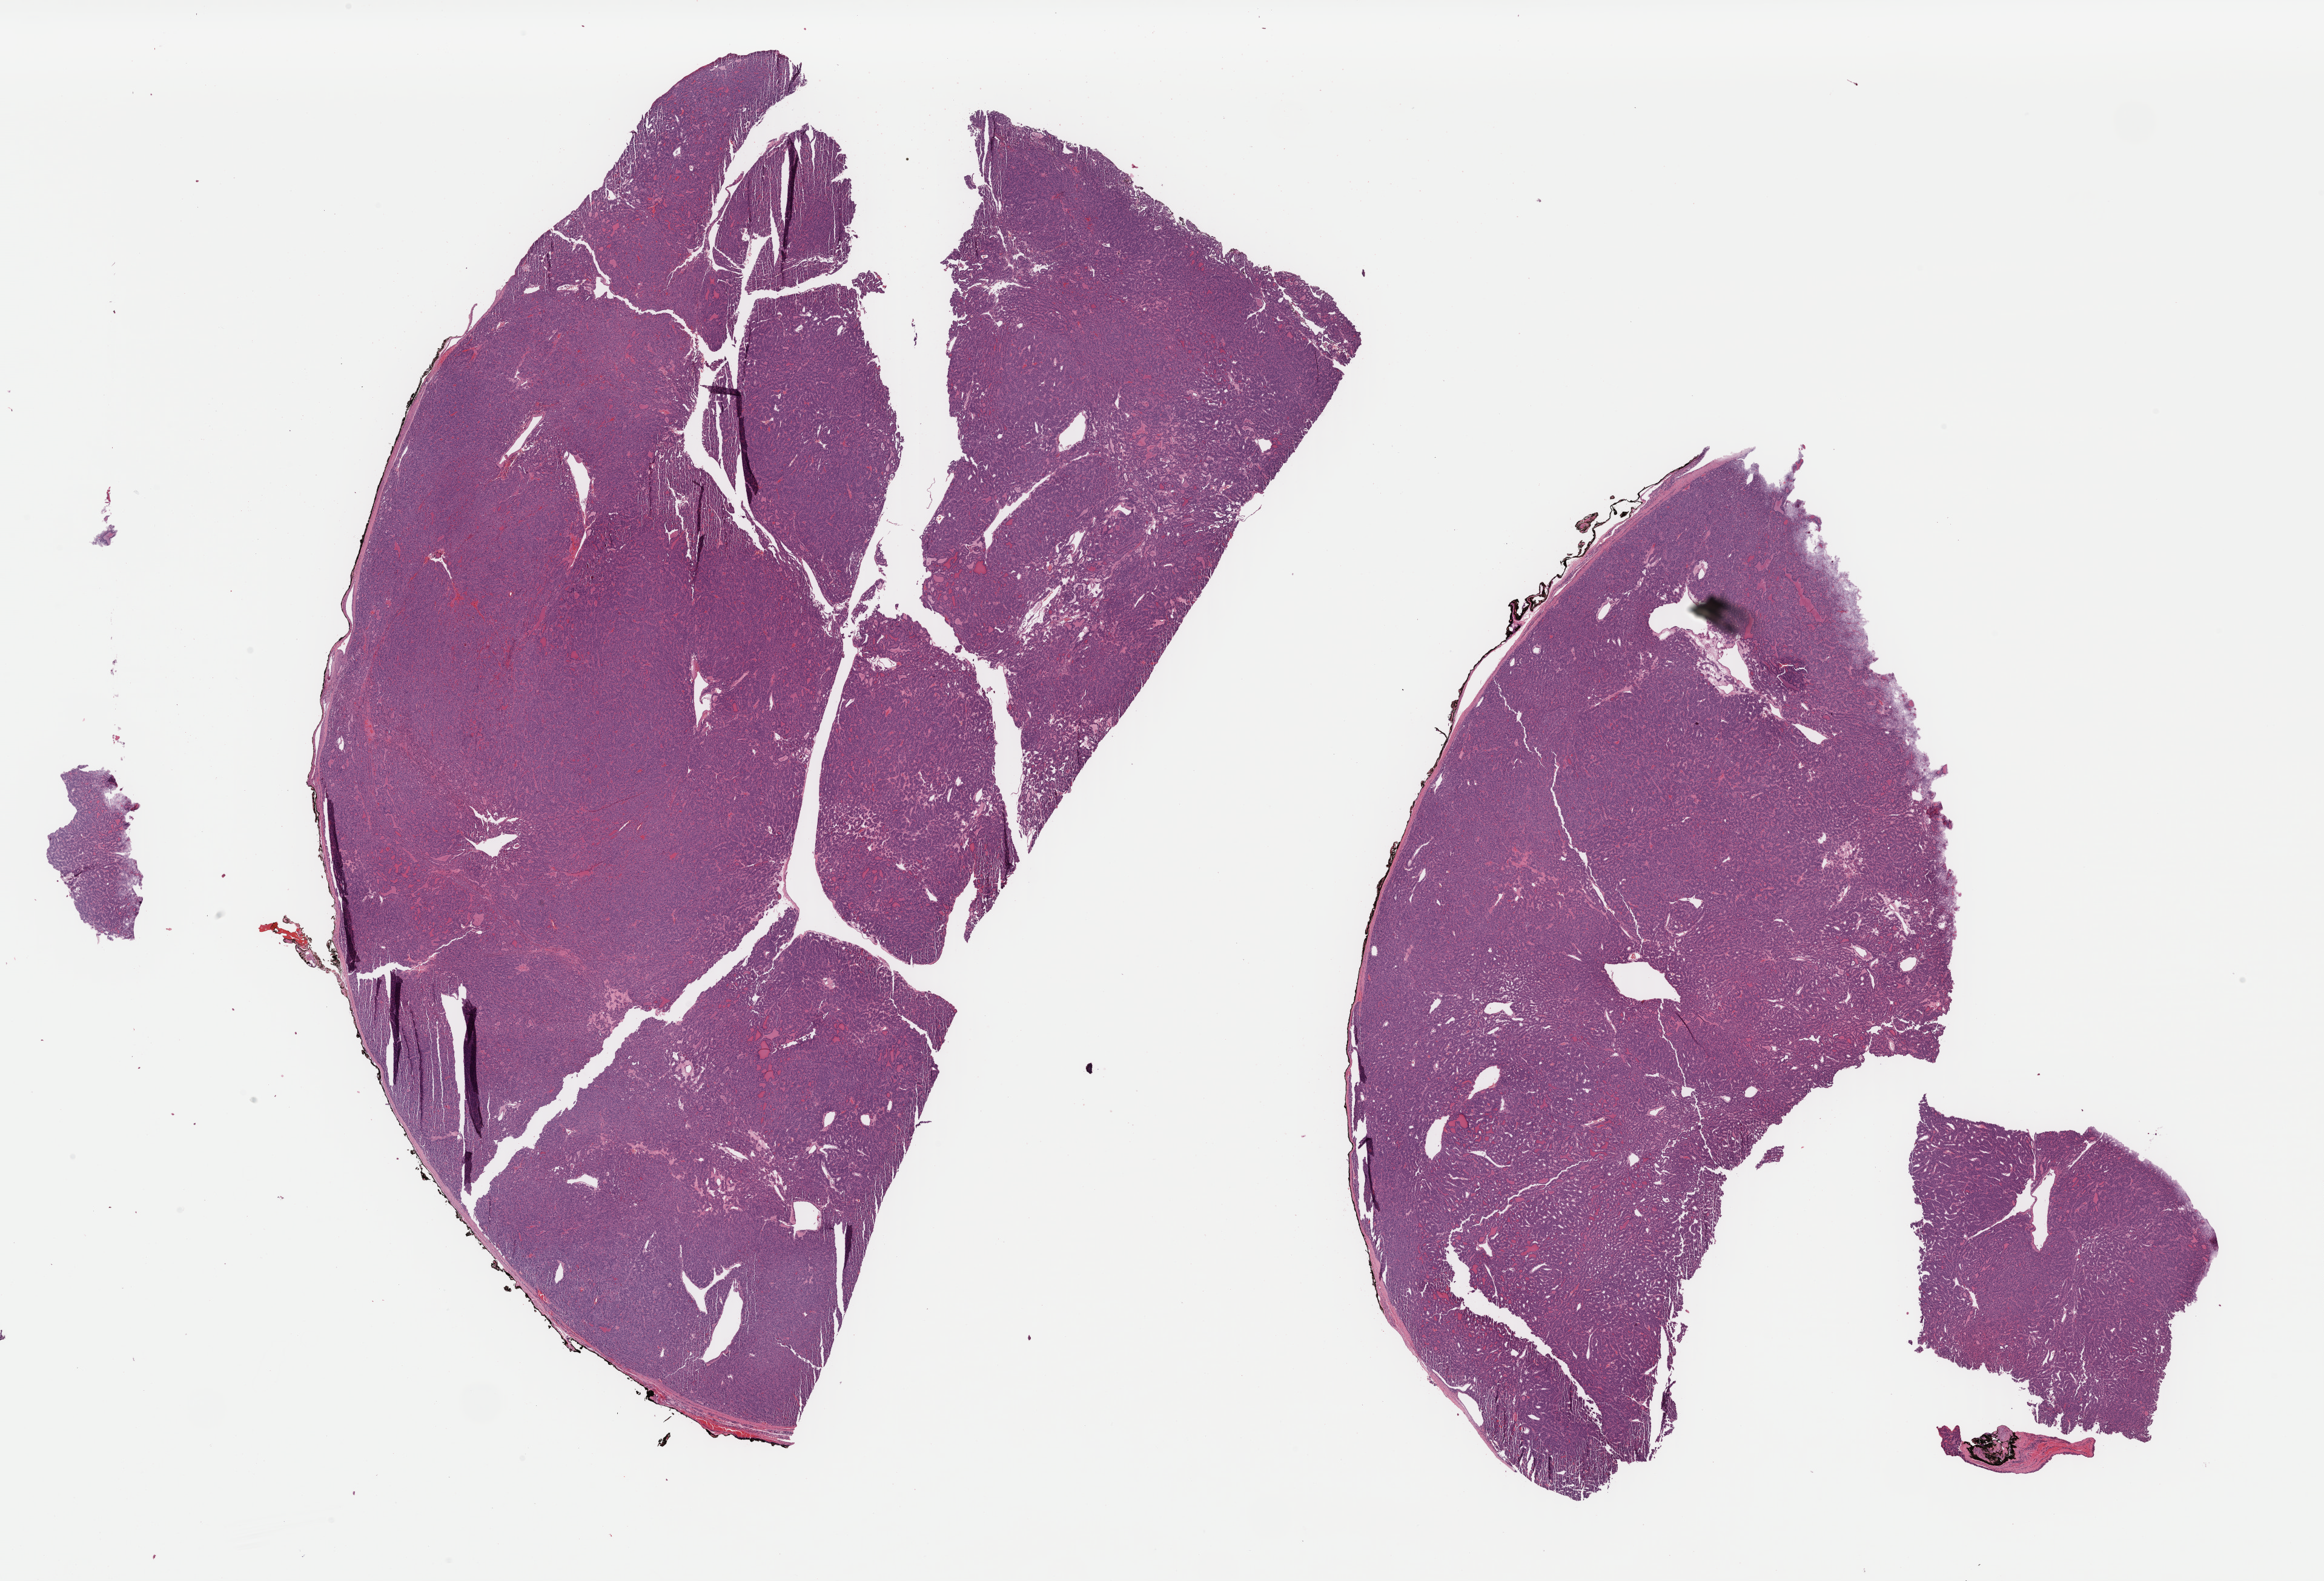
Whole-slide histology image, H&E-stained, low-resolution overview of the scanned area, about 30.3 x 20.6 mm (from a 40x scan), formalin-fixed paraffin-embedded (FFPE) diagnostic section, thyroid, primary tumour sample. Female patient; age at initial diagnosis 51 years.
Histologic diagnosis: Papillary carcinoma, follicular variant (thyroid gland). AJCC pathologic stage: II. TNM: T2 N0 M0.